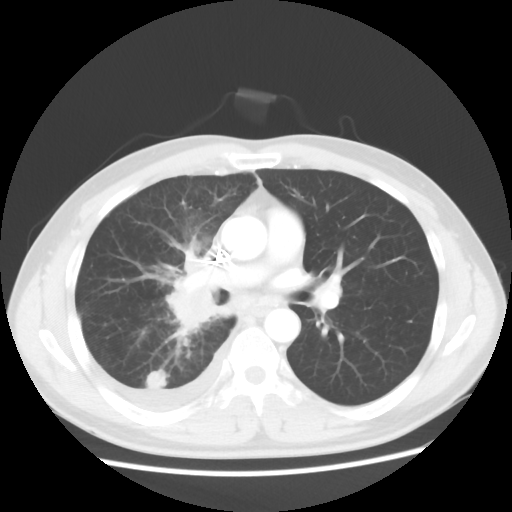
Chest CT, one axial slice. Slice 30 of 56 in the series (ordered by position). 120 kVp. Lung window (W 1500 / L -600 HU). 5 mm slice thickness. 512 × 512 image matrix, field of view 360 × 360 mm. Patient: male, 46 years. From the clinical record (not read from this slice): clinical TNM (as recorded): T2 N3 M1.
Annotated regions visible in this slice (rectangle marked by the reading radiologist):
- lung tumour (recorded histology: adenocarcinoma): bounding box [x1, y1, x2, y2] px = [154, 253, 220, 337]